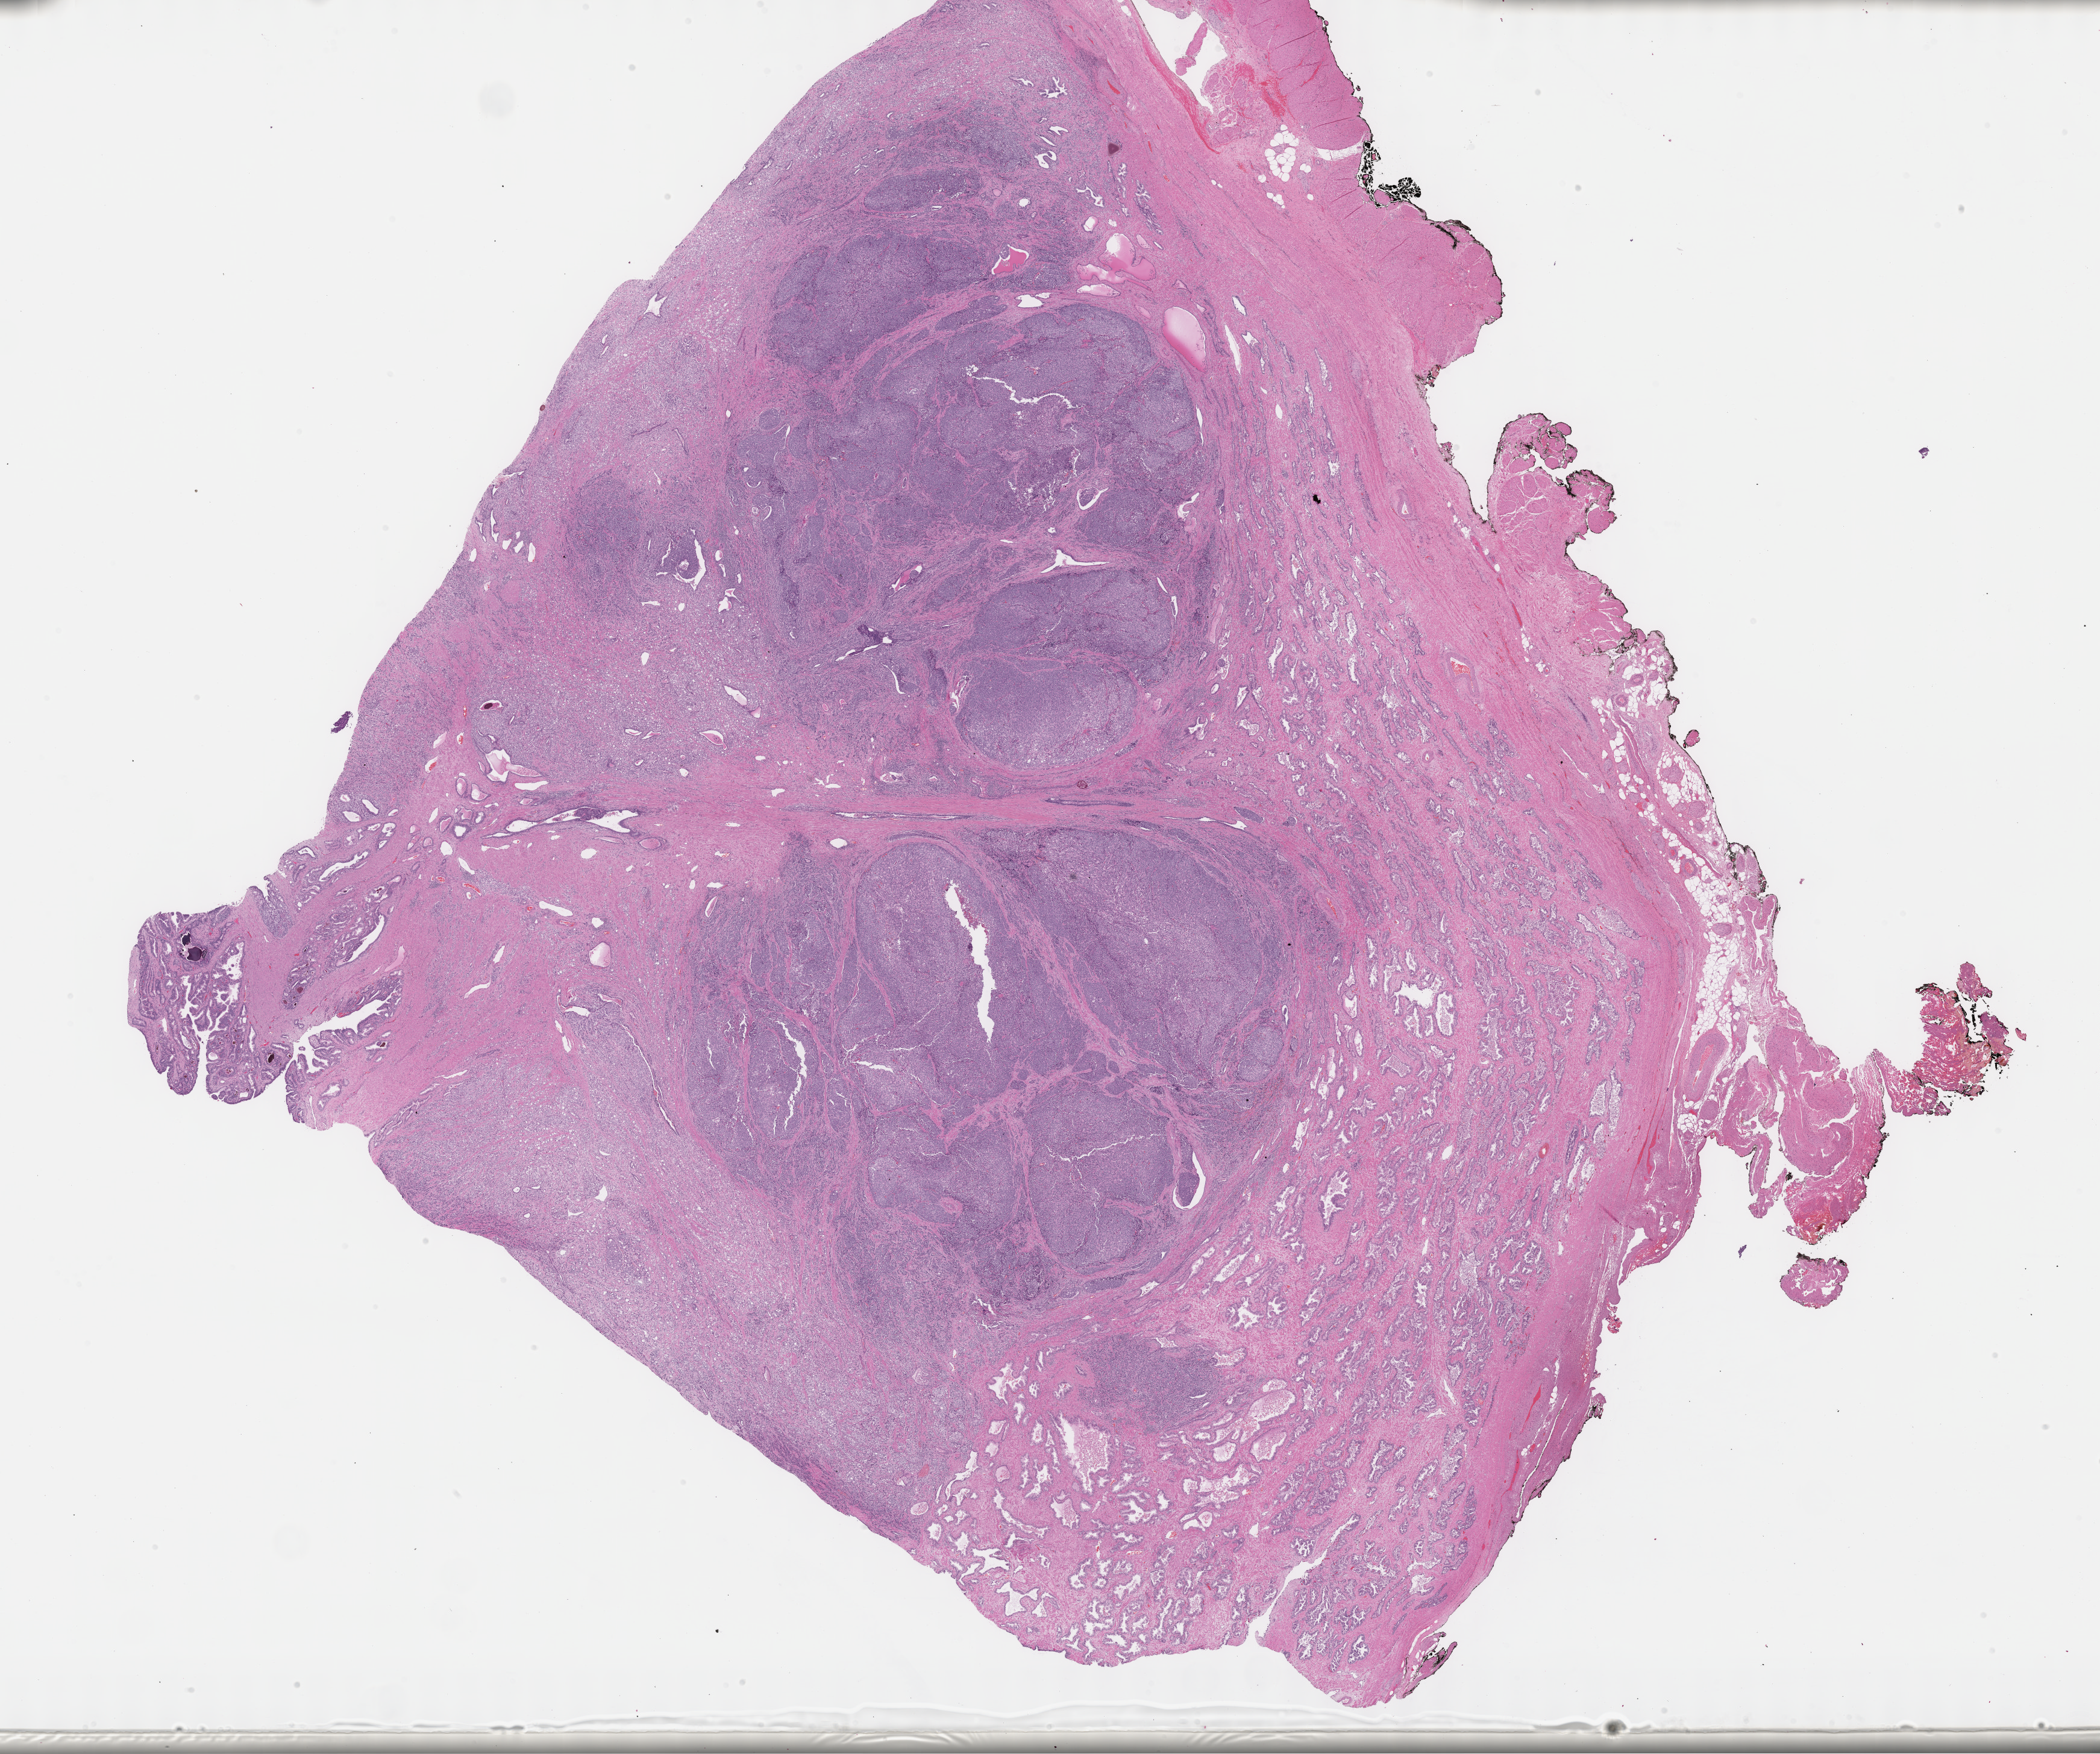
H&E whole-slide image — shown as a low-resolution overview of the whole scanned area (about 28.2 x 23.5 mm); formalin-fixed paraffin-embedded (FFPE) diagnostic section; prostate, primary tumour sample. Male, age 51 years at initial diagnosis. Gleason score: 9 (5+4).
Diagnosis: Adenocarcinoma, NOS (prostate gland). Lymph nodes positive (case pathology): 2 of 22 examined.